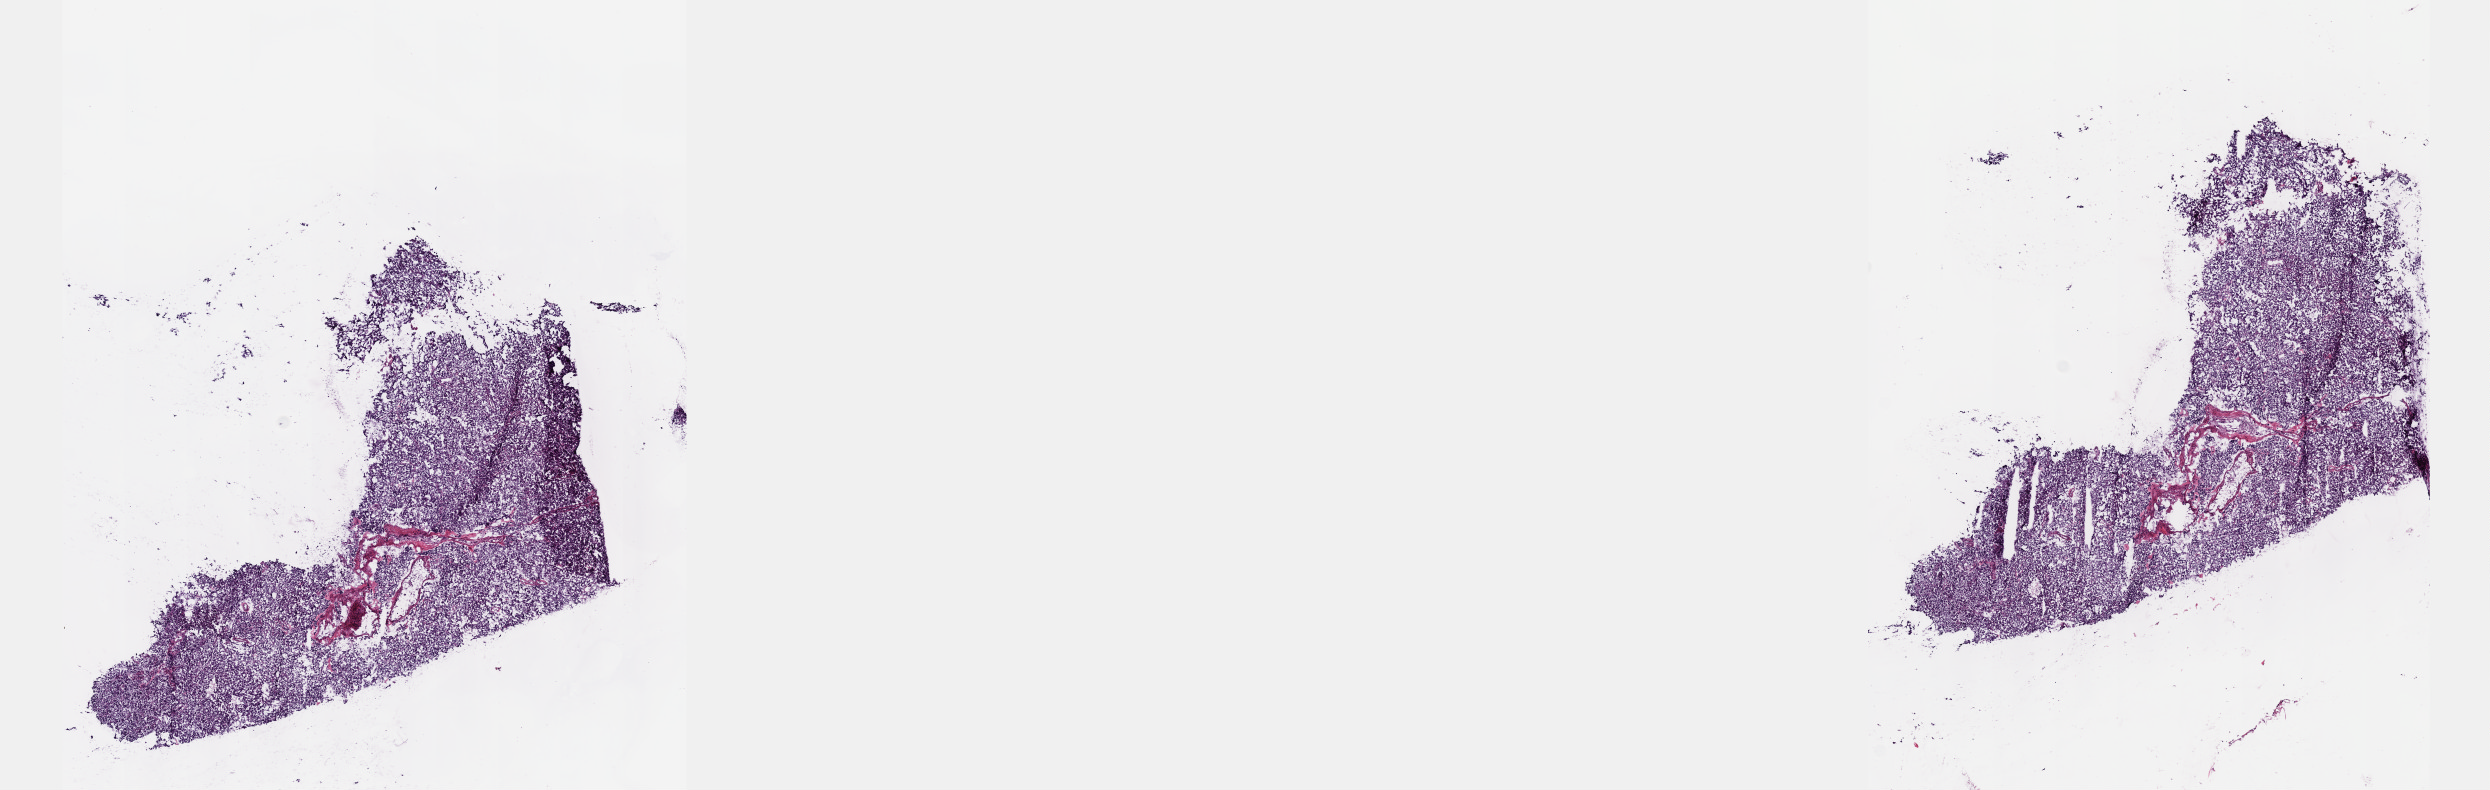
Whole-slide histology image, Hematoxylin and eosin (H&E) stained, whole scanned area (about 20.1 x 6.4 mm, slide scanned at 40x) shown as a low-resolution overview. Frozen section. Adrenal gland, primary tumour sample. Patient: male, age at initial diagnosis 63 years. Pathologist review of this section (percent, as recorded): tumour cells 95%, tumour nuclei 95%, normal cells 0%, stromal cells 5%, necrosis 0%. Inflammatory infiltration, as recorded: lymphocyte infiltration 0%, monocyte infiltration 0%, neutrophil infiltration 0%.
Diagnosis: Pheochromocytoma, NOS.